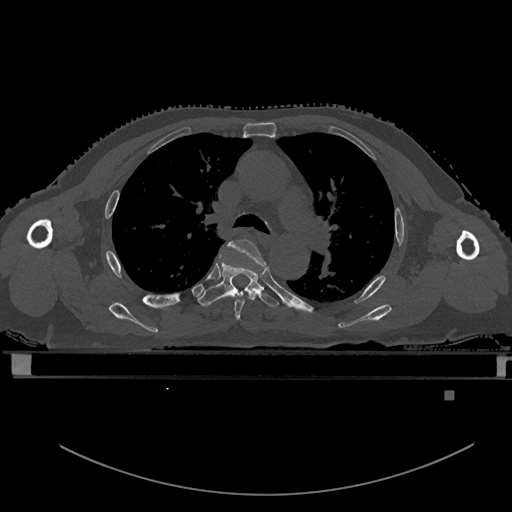
CT including the spine, one axial slice; position 377 of 969 along the scan axis; bone window (W 1800 / L 400 HU); 0.5 mm slice thickness; 512 × 512 image matrix, field of view 456 × 456 mm. Male patient, age 82 years. From the clinical record (not read from this slice): primary cancer: prostate; vertebrae with lytic lesions (as recorded): T11, T9, T8, T2.
Structures marked on this image (semi-automatically segmented with operator editing):
- T4 vertebra: bounding box [x1, y1, x2, y2] px = [223, 239, 266, 320]
- T5 vertebra: [198, 254, 279, 308]